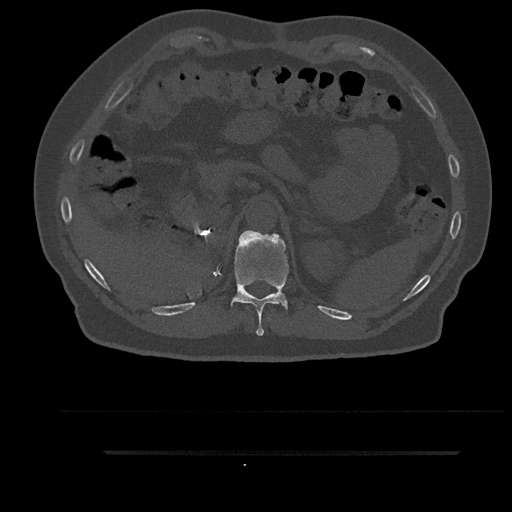
CT including the spine, one axial slice. Slice 297 of 797 in the series (ordered by position). 120 kVp. Bone window (W 1800 / L 400 HU). 0.5 mm slice thickness. 512 × 512 image matrix. Patient: male, 63 years. Case-level facts recorded for this patient, not image findings: primary cancer: renal; vertebrae with lytic lesions (as recorded): T8.
Structures marked on this image (semi-automatically segmented with operator editing):
- T11 vertebra: box from (x=225, y=230) to (x=290, y=336) px